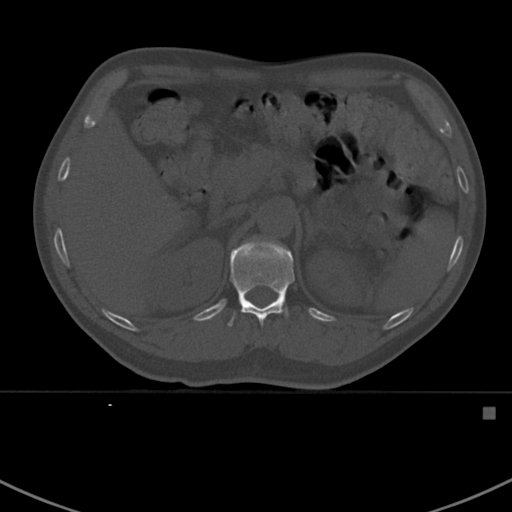
CT including the spine, one axial slice; slice 328 of 412 in the series (ordered by position); reconstruction kernel Br40s; 120 kVp; bone window (W 1800 / L 400 HU); 1.5 mm slice thickness; 512 × 512 image matrix, field of view 358 × 358 mm. Male patient, age 59 years. Case-level facts recorded for this patient, not image findings: primary cancer: prostate.
Structures marked on this image (semi-automatically segmented with operator editing):
- T12 vertebra: bounding box (x1, y1, x2, y2) in pixels: (228, 239, 295, 327)